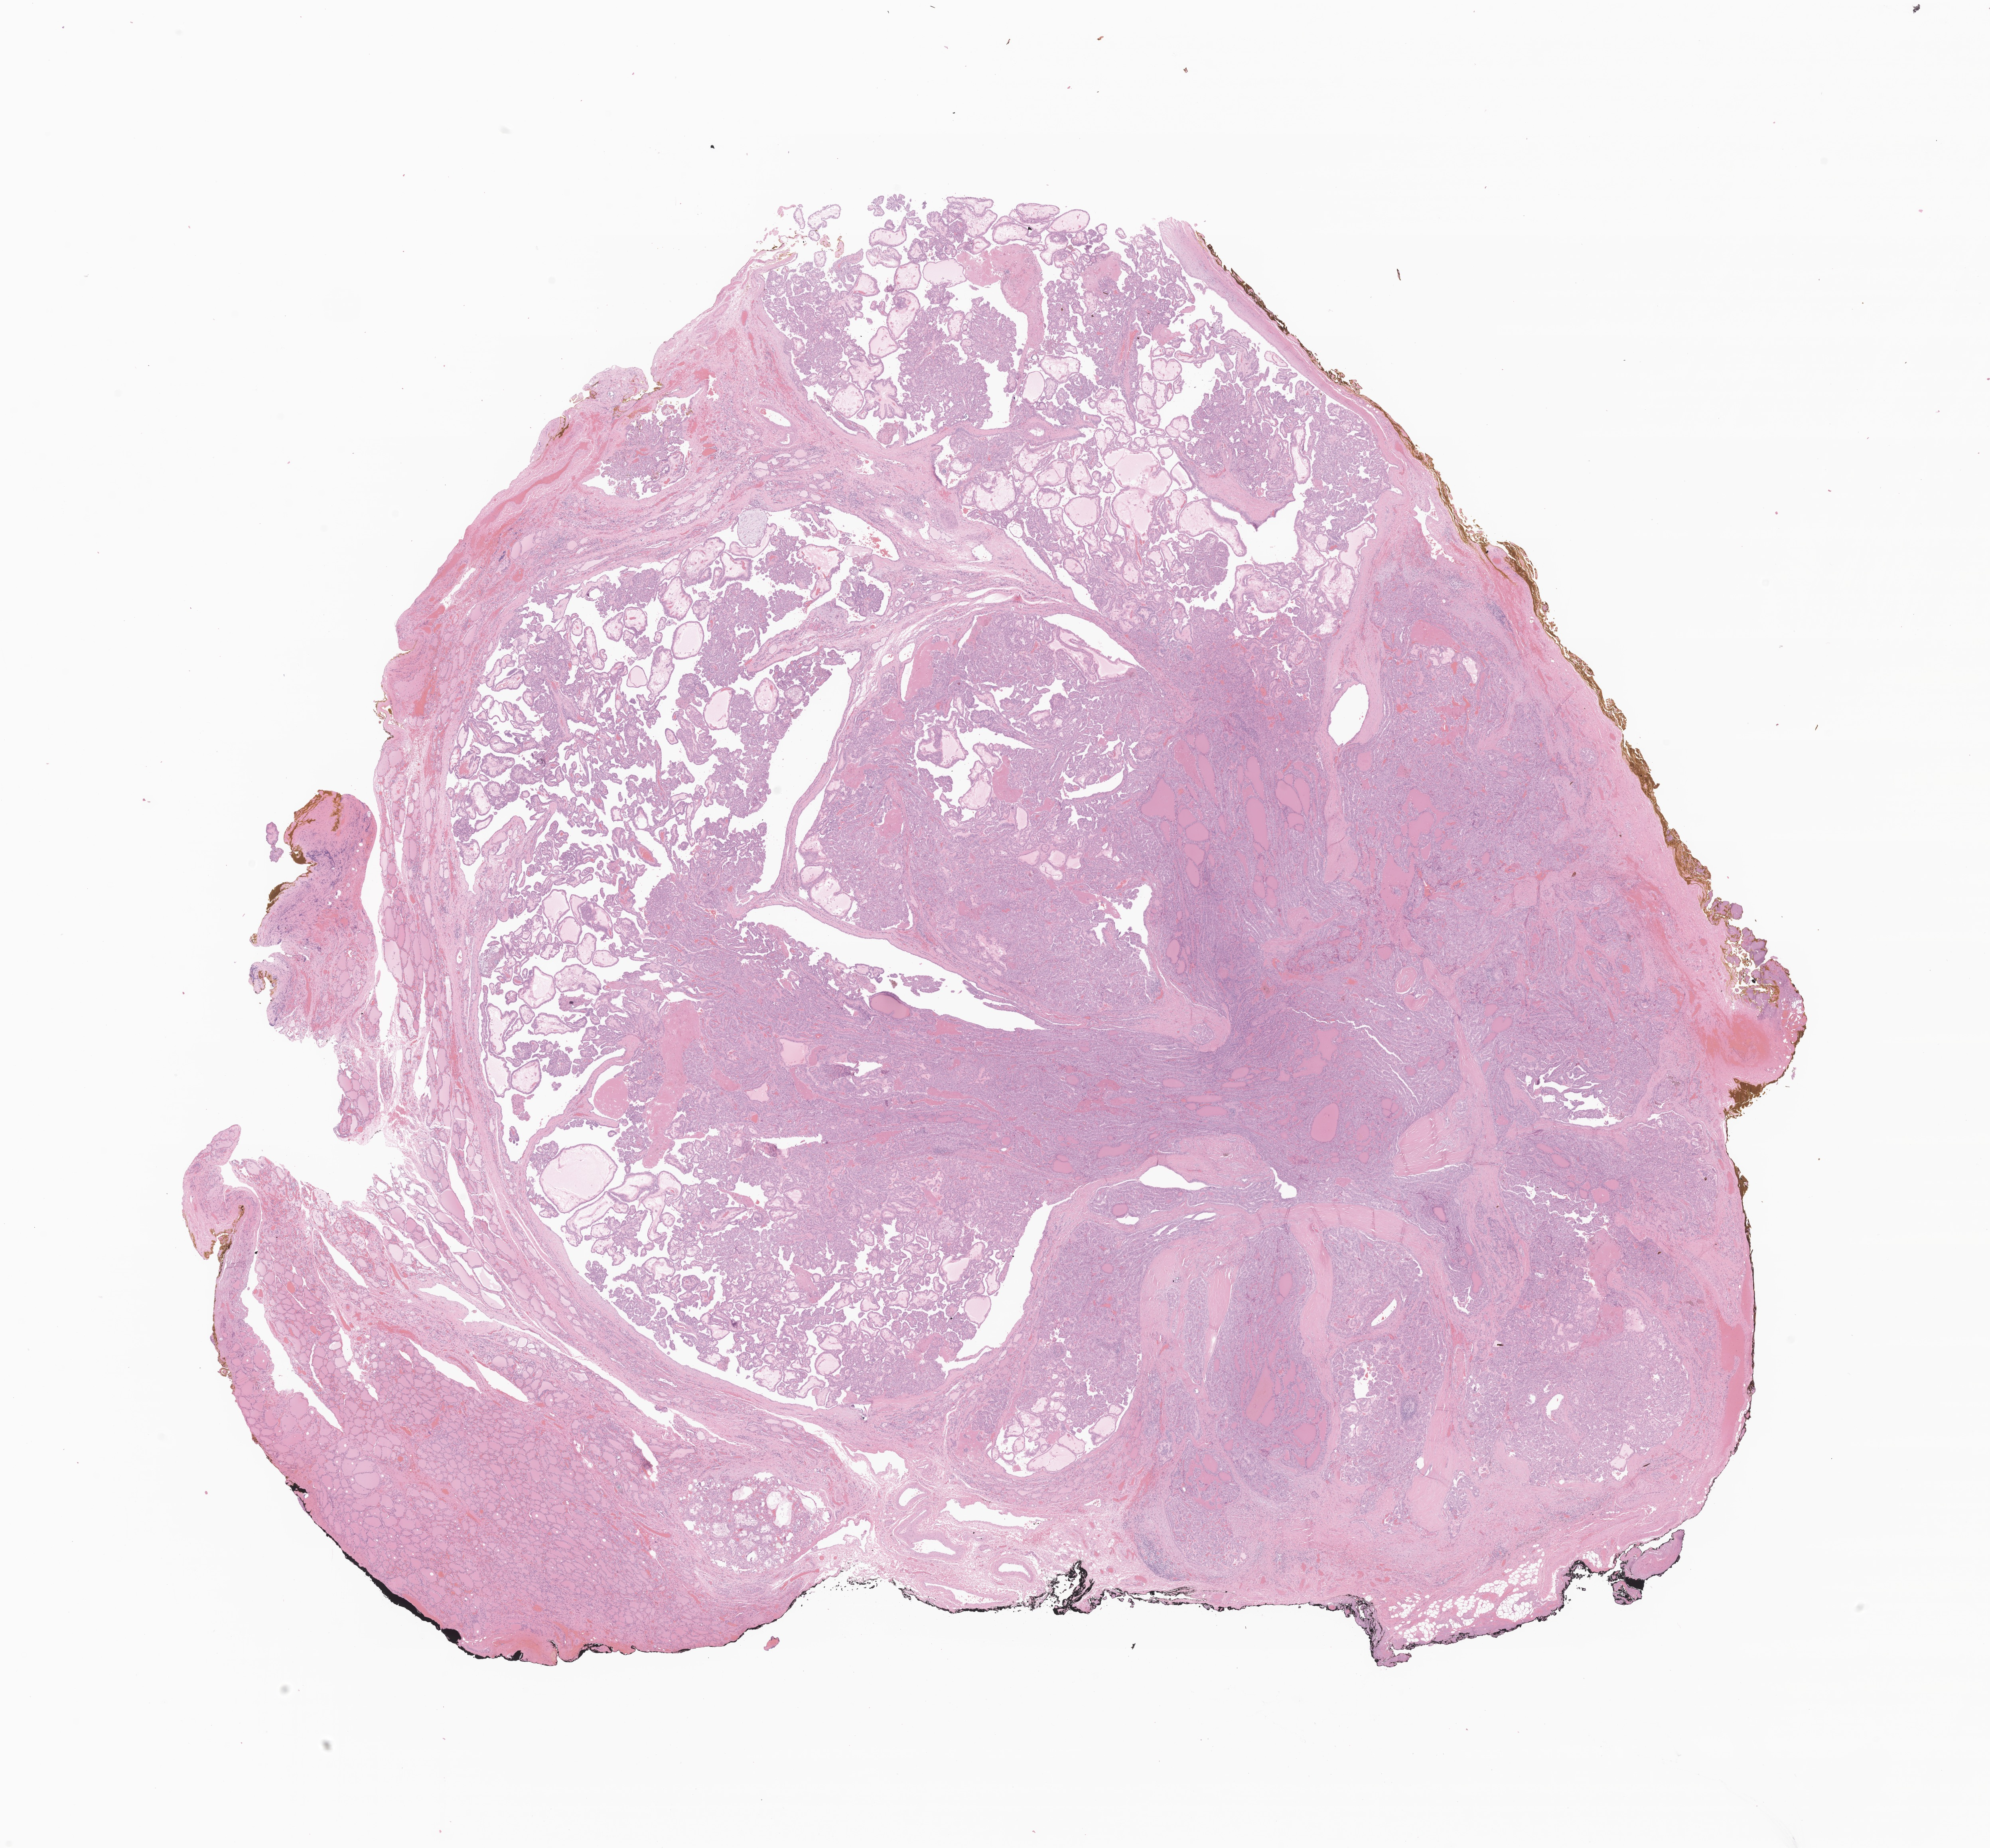
Digitized hematoxylin and eosin (H&E)-stained section of tumor tissue from the thyroid, shown as a low-resolution overview of the whole scanned area (about 21.0 x 19.5 mm); formalin-fixed paraffin-embedded section. Female patient, age 192 months (16 years).
Diagnosis: Papillary carcinoma, NOS.